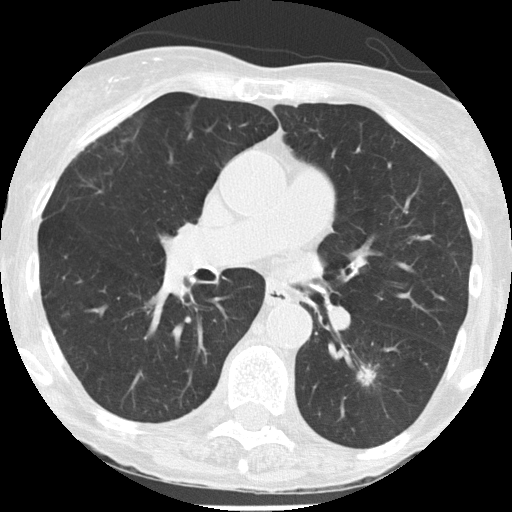
Axial slice from a low-dose chest CT screening exam; third annual screen; lung window (W 1500 / L -600 HU); lung (sharp) reconstruction kernel (FC51); slice 75 of 146 in the series. Female, age 68 years at enrolment. Former smoker at enrolment.
Expert-annotated lung lesion, box from (x=337, y=349) to (x=398, y=403) px. Reader record for this screening exam (exam-level; its link to the box is not recorded): non-calcified nodule or mass ≥4 mm, left lower lobe, 11 × 9 mm, spiculated (stellate) margins, soft tissue attenuation, pre-existing on the prior screen: yes; interval growth: yes. Lung cancer was diagnosed 164 days after this screen: non-small cell carcinoma, left lower lobe, poorly differentiated (G3), stage IA (AJCC 6th edition), 10 mm at pathology.